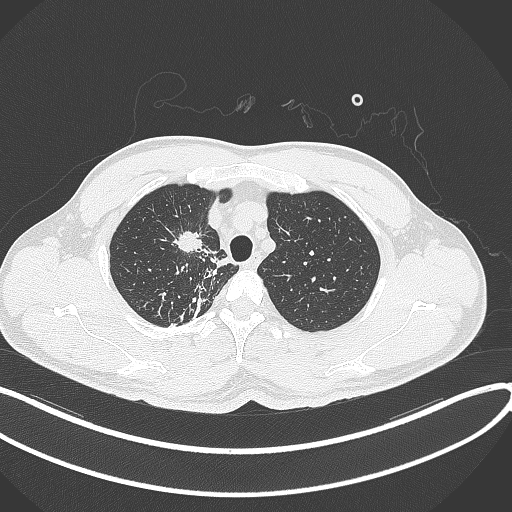
Chest CT, one axial slice; slice 308 of 391 in the series (ordered by position); lung window (W 1500 / L -600 HU); 512 × 512 image matrix, field of view 400 × 400 mm. Male patient, age 48 years. Case-level facts recorded for this patient, not image findings: clinical TNM (as recorded): T1c N1 M1.
Outlined on this slice (bounding box drawn by a radiologist):
- lung tumour (recorded histology: adenocarcinoma): bounding box (x1, y1, x2, y2) in pixels: (171, 226, 206, 256)